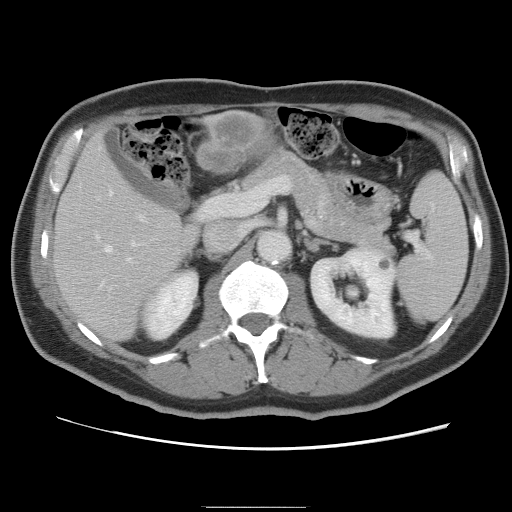
Contrast-enhanced abdominal CT, one axial slice. Position 43 of 87 along the scan axis. 120 kVp. Intravenous contrast given. Soft-tissue window (W 400 / L 40 HU). 5 mm slice thickness. 512 × 512 image matrix, field of view 363 × 363 mm. Male patient, age 63 years. Case-level facts recorded for this patient, not image findings: diagnosis: colorectal cancer liver metastases, imaged before liver resection; multiple liver metastases: no; largest metastasis: 9 cm.
Outlined on this slice (manually delineated by an expert):
- hepatic veins: bounding box (x1, y1, x2, y2) in pixels: (97, 192, 135, 283)
- liver: (54, 112, 279, 341)
- planned liver remnant (the part of the liver to remain after resection): (54, 148, 195, 342)
- portal vein (with intrahepatic branches): (96, 196, 204, 291)
- liver metastasis: (202, 118, 277, 170)